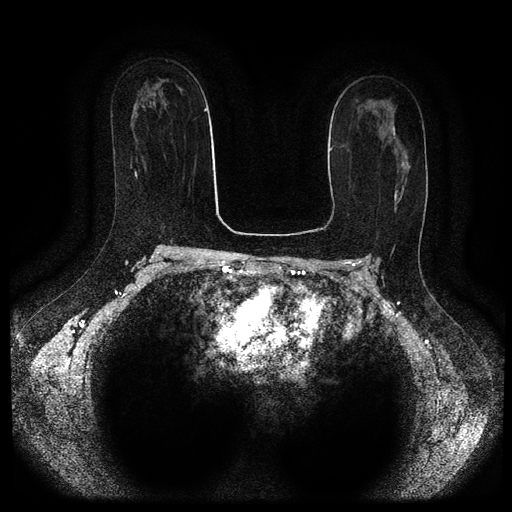
Breast MRI (dynamic contrast-enhanced, multi-phase), one axial slice; slice 62 of 116 in the series (ordered by position); dynamic contrast-enhanced series, time point 2 of 5 at this slice position (early post-contrast); 1.5 T; TE 2.7 ms, TR 5.4 ms; 512 × 512 image matrix, field of view 340 × 340 mm. Patient: female, 47 years.
Annotated regions visible in this slice (semi-automatically segmented with operator editing):
- breast lesion (labelled benign in the annotation): bounding box (x1, y1, x2, y2) in pixels: (392, 126, 396, 139)